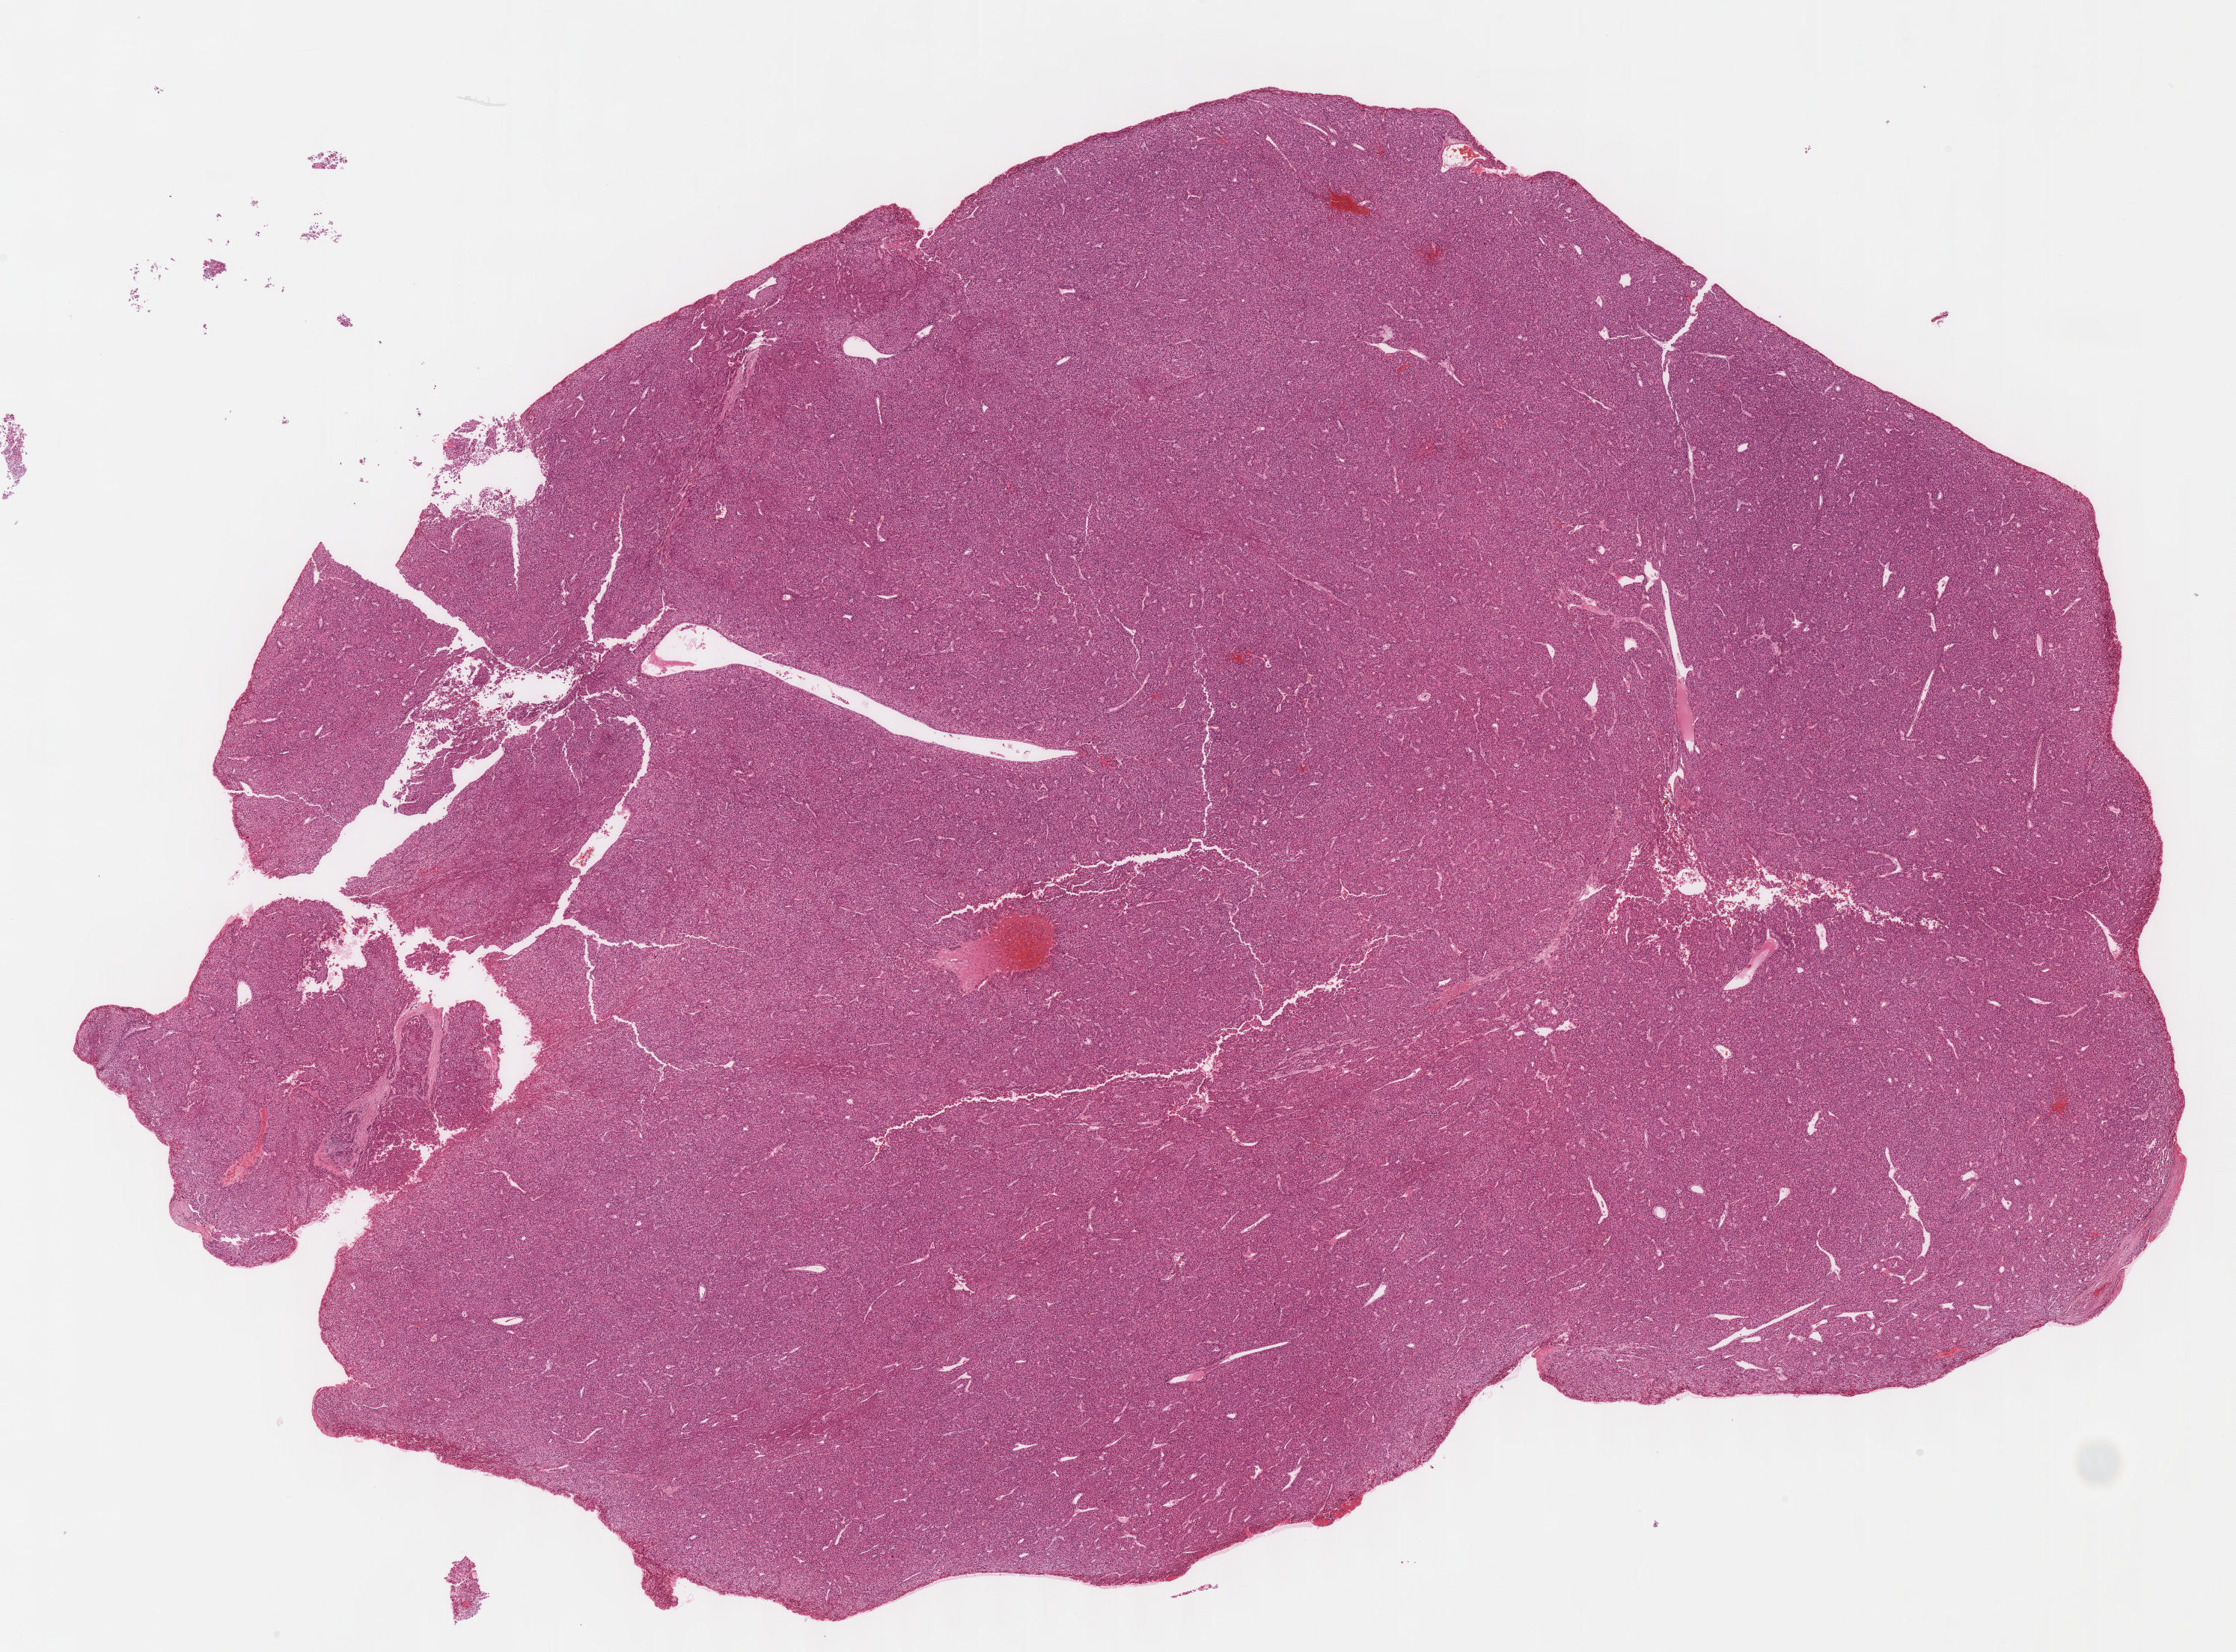
Whole-slide histology image, Hematoxylin and eosin (H&E) stained, whole scanned area (about 24.1 x 17.8 mm) shown as a low-resolution overview, formalin-fixed paraffin-embedded (FFPE) diagnostic section, primary tumour sample from the liver. Female, age 59 years at initial diagnosis.
Histologic diagnosis: Hepatocellular carcinoma, NOS.